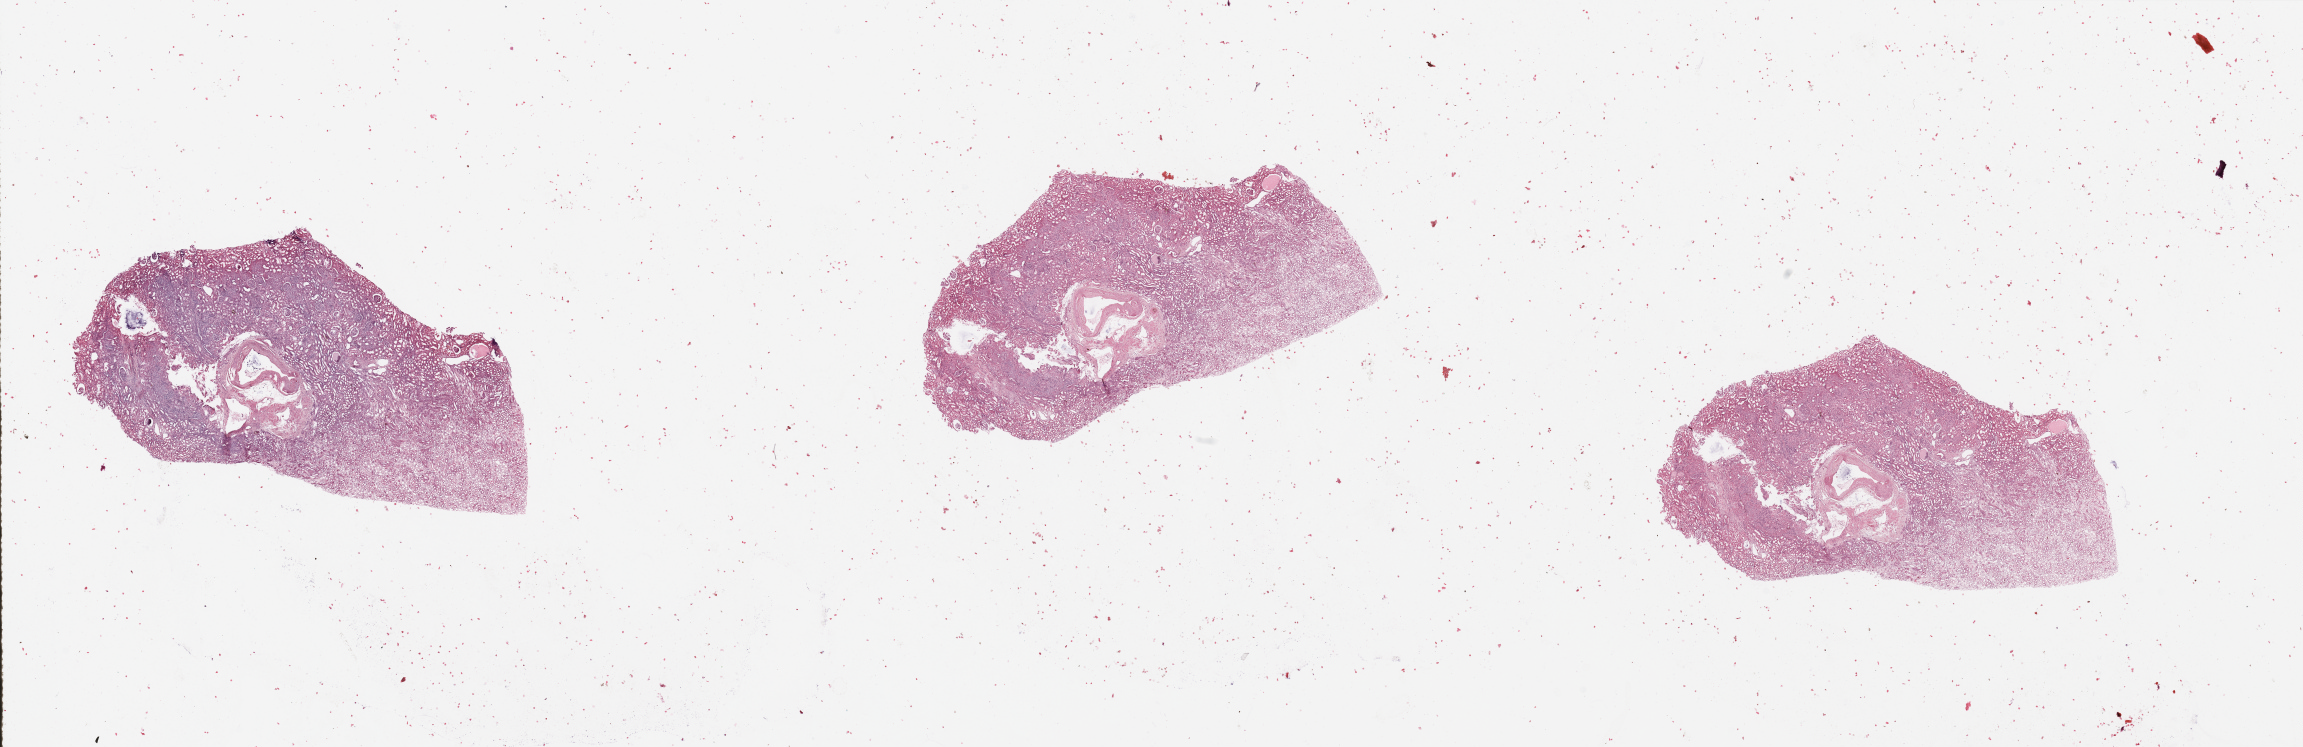
Digitized H&E-stained tissue section (whole slide), a low-resolution overview of the entire scanned area, about 36.4 x 11.8 mm. Normal (non-tumour) tissue sample, sampled site: kidney. 69-year-old female patient.
This section: normal (non-tumour) tissue from the same patient. Patient diagnosis: Renal cell carcinoma, NOS.